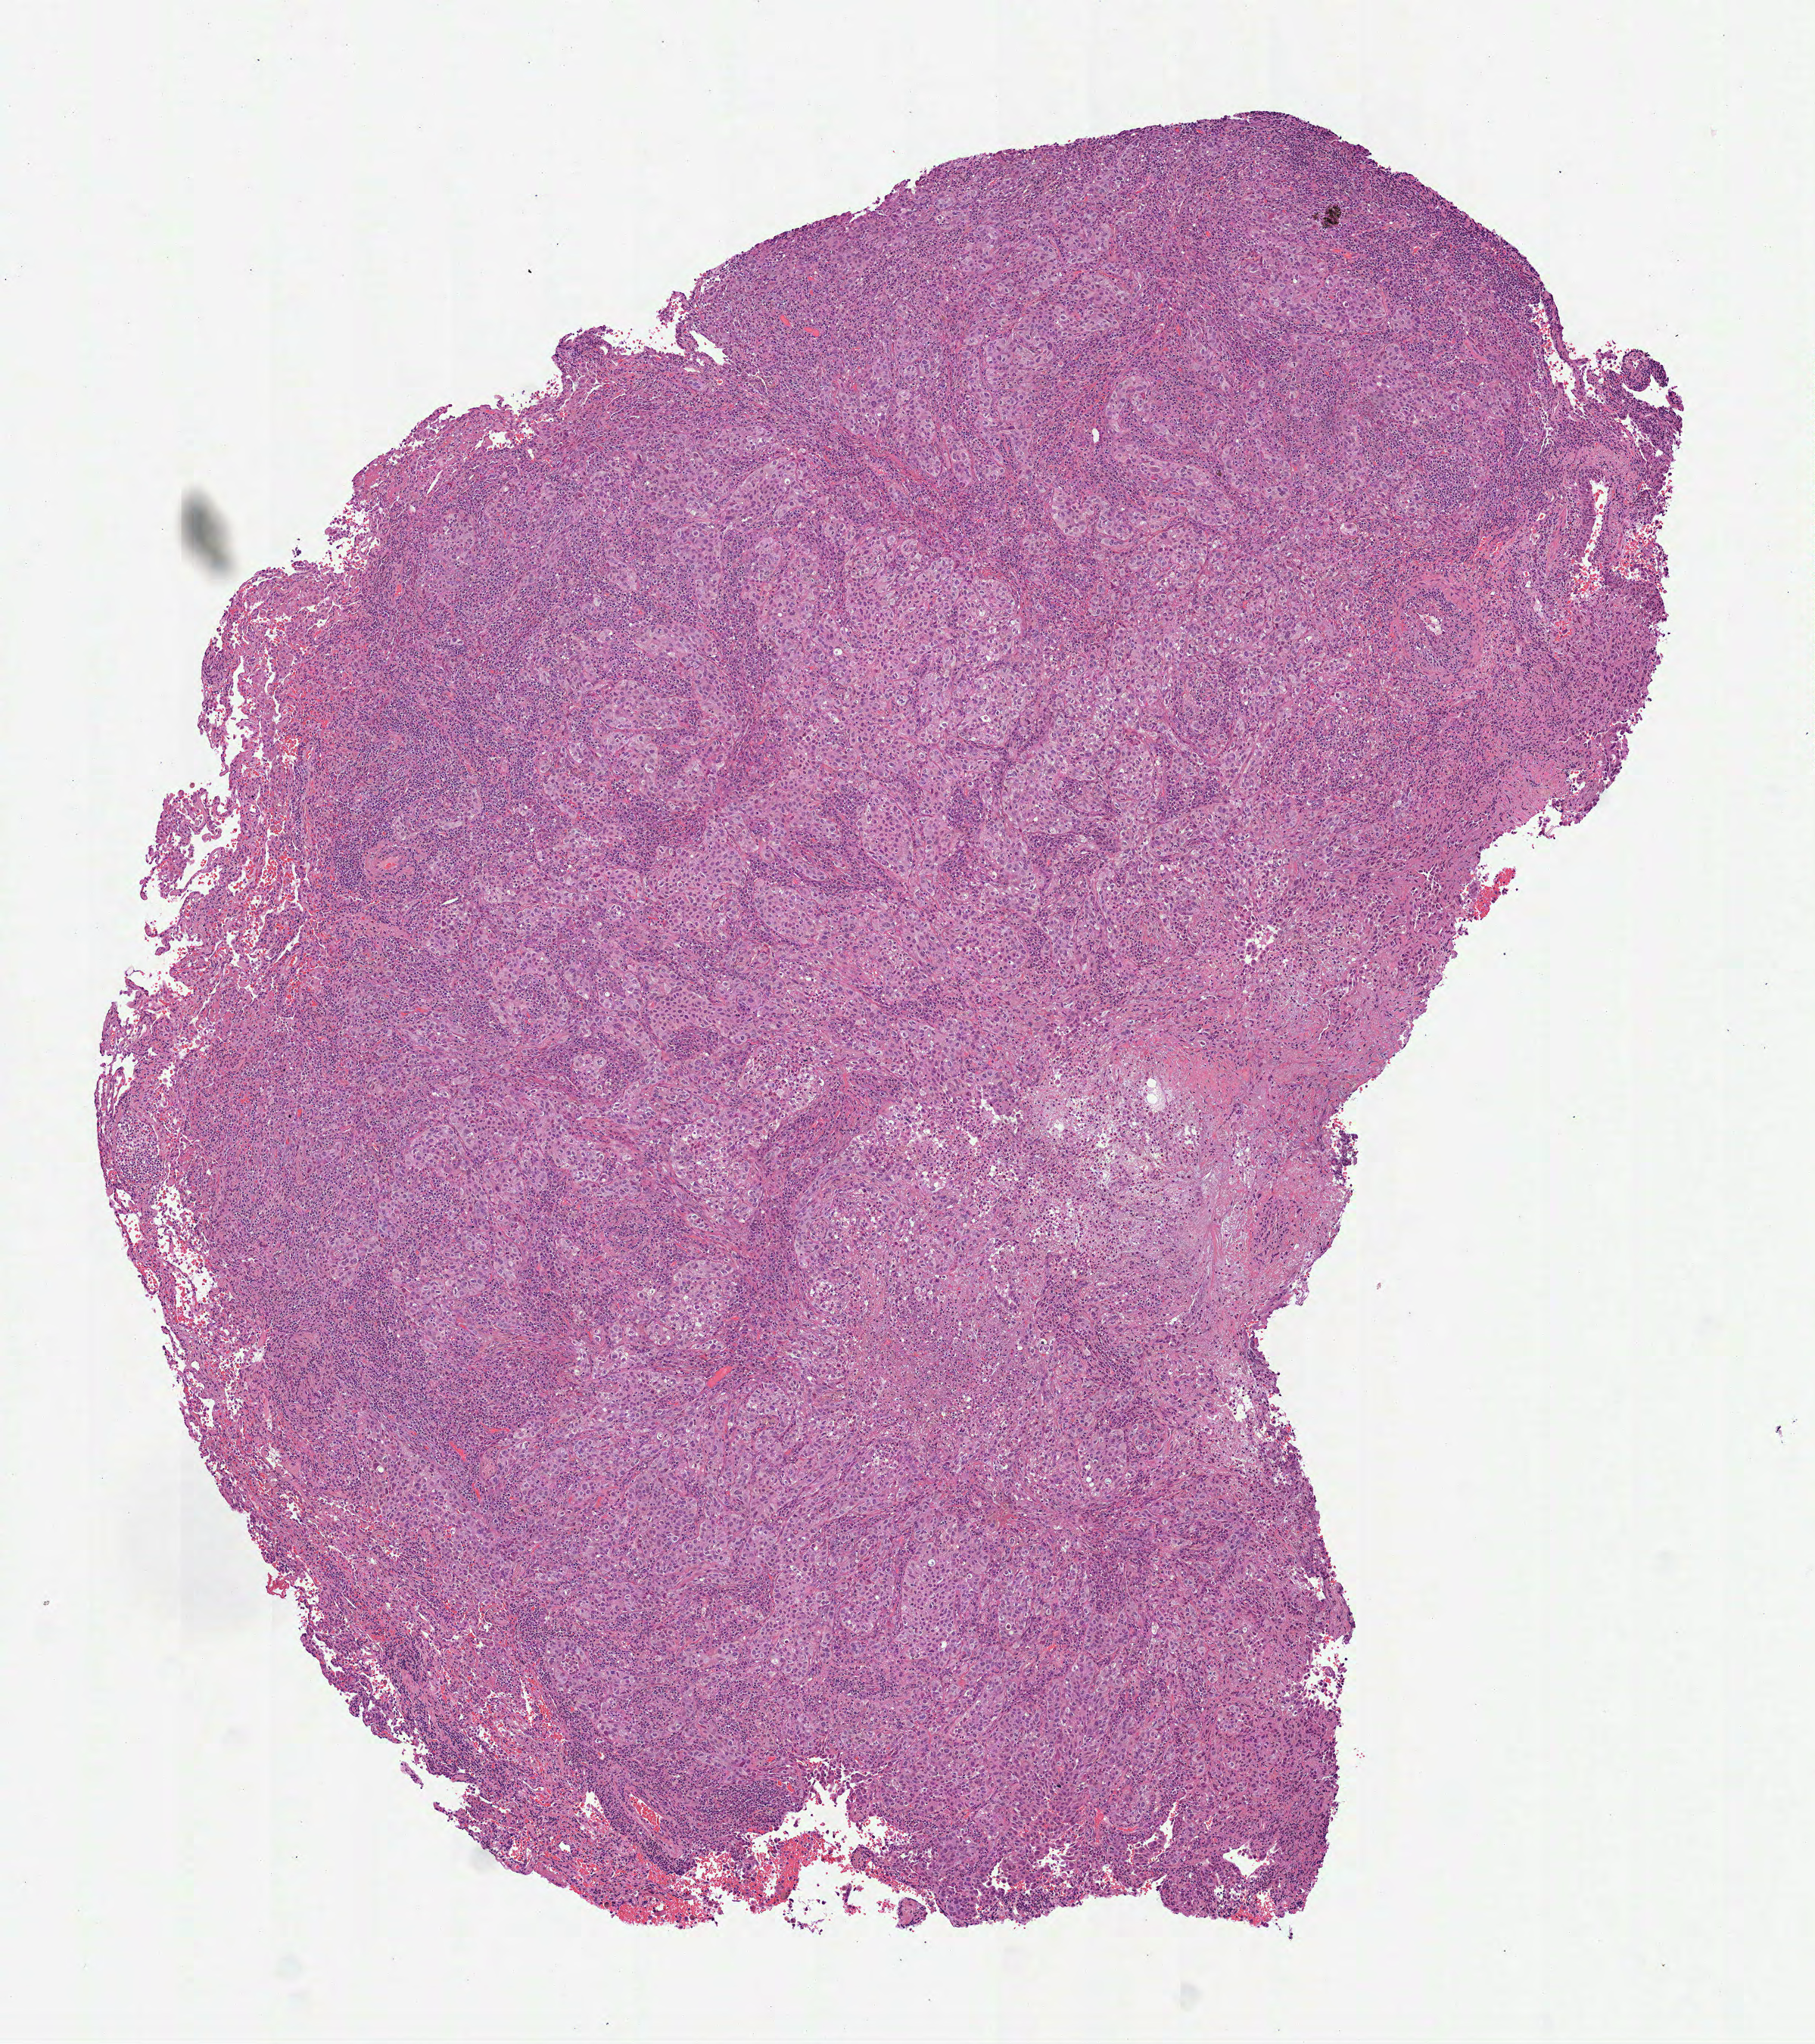
Whole-slide histology image, H&E-stained — low-resolution overview of the scanned area, about 4.8 x 5.4 mm (from a 40x scan), formalin-fixed paraffin-embedded (FFPE) diagnostic section, sample: primary tumour, lung. Patient: male, age at initial diagnosis 56 years.
Diagnosis: Adenocarcinoma, NOS (upper lobe, lung). AJCC pathologic stage: IA (7th edition).